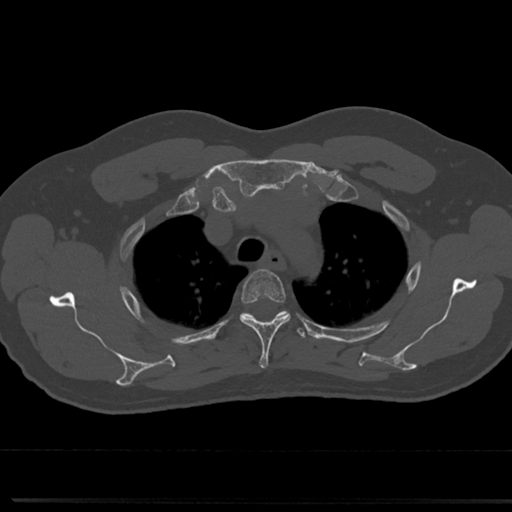
CT including the spine, one axial slice. Position 581 of 817 along the scan axis. Reconstruction kernel Br40s/3. 120 kVp. Bone window (W 1800 / L 400 HU). 512 × 512 image matrix, field of view 355 × 355 mm. Patient: male, 61 years. From the clinical record (not read from this slice): primary cancer: prostate.
Structures marked on this image (semi-automatic segmentation, software-assisted and operator-edited):
- T3 vertebra: bounding box [x1, y1, x2, y2] px = [239, 270, 290, 369]
- T4 vertebra: [222, 309, 309, 343]